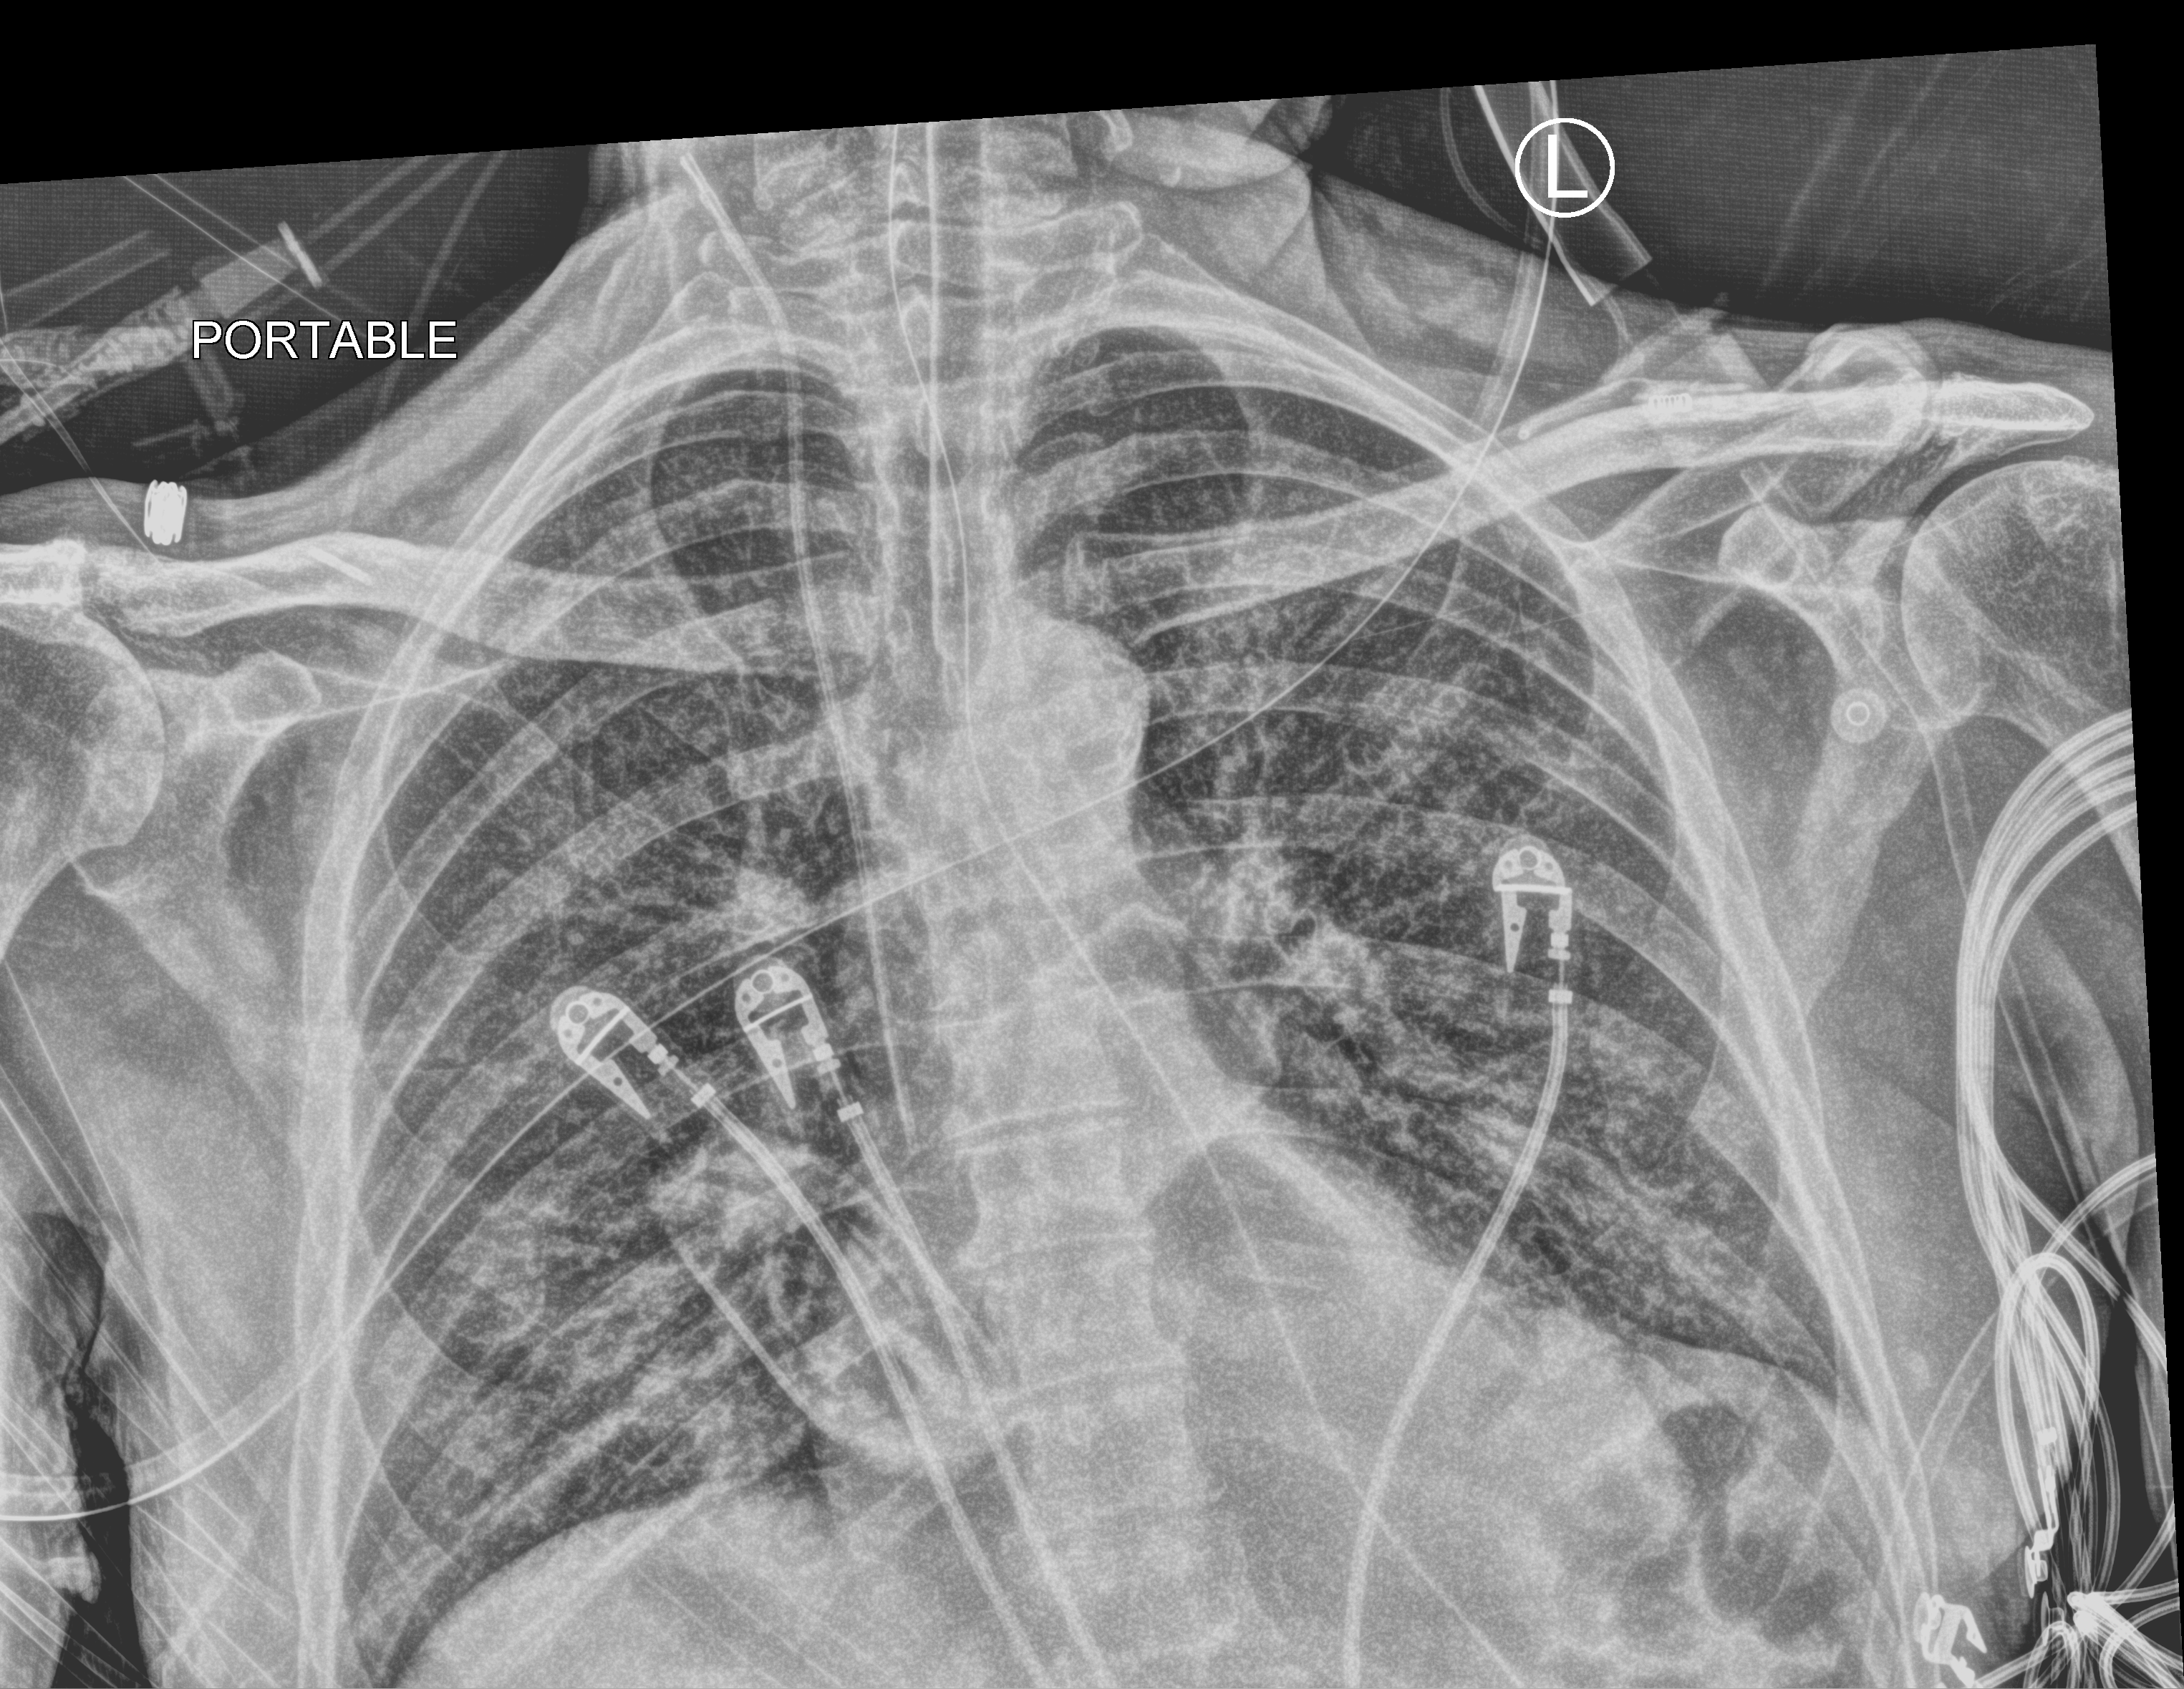
Chest X-ray (portable), anteroposterior (AP) projection. Patient hospitalised with COVID-19; male, aged 75–90 years.
Admission-level facts for this patient (not findings on this image; timing relative to this image not recorded): admitted to intensive care during this hospital stay: yes; length of hospital stay: 10 days.